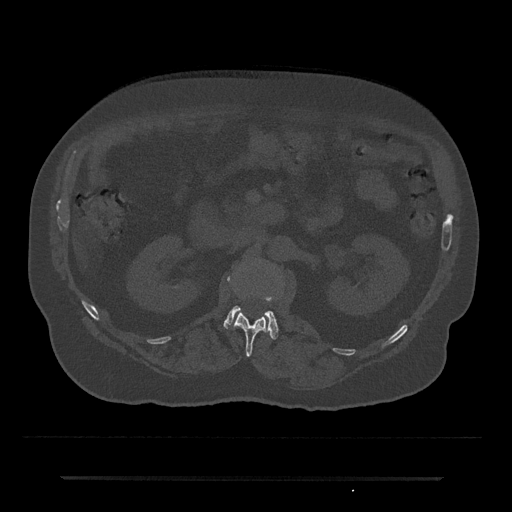
CT including the spine, one axial slice; position 43 of 797 along the scan axis; reconstruction kernel Br40s/3; bone window (W 1800 / L 400 HU); 0.5 mm slice thickness; 512 × 512 image matrix, field of view 437 × 437 mm. Male patient, age 69 years. Case-level facts recorded for this patient, not image findings: primary cancer: prostate.
Annotated regions visible in this slice (semi-automatic segmentation, software-assisted and operator-edited):
- L1 vertebra: bounding box (x1, y1, x2, y2) in pixels: (227, 276, 268, 357)
- L2 vertebra: (224, 297, 278, 339)